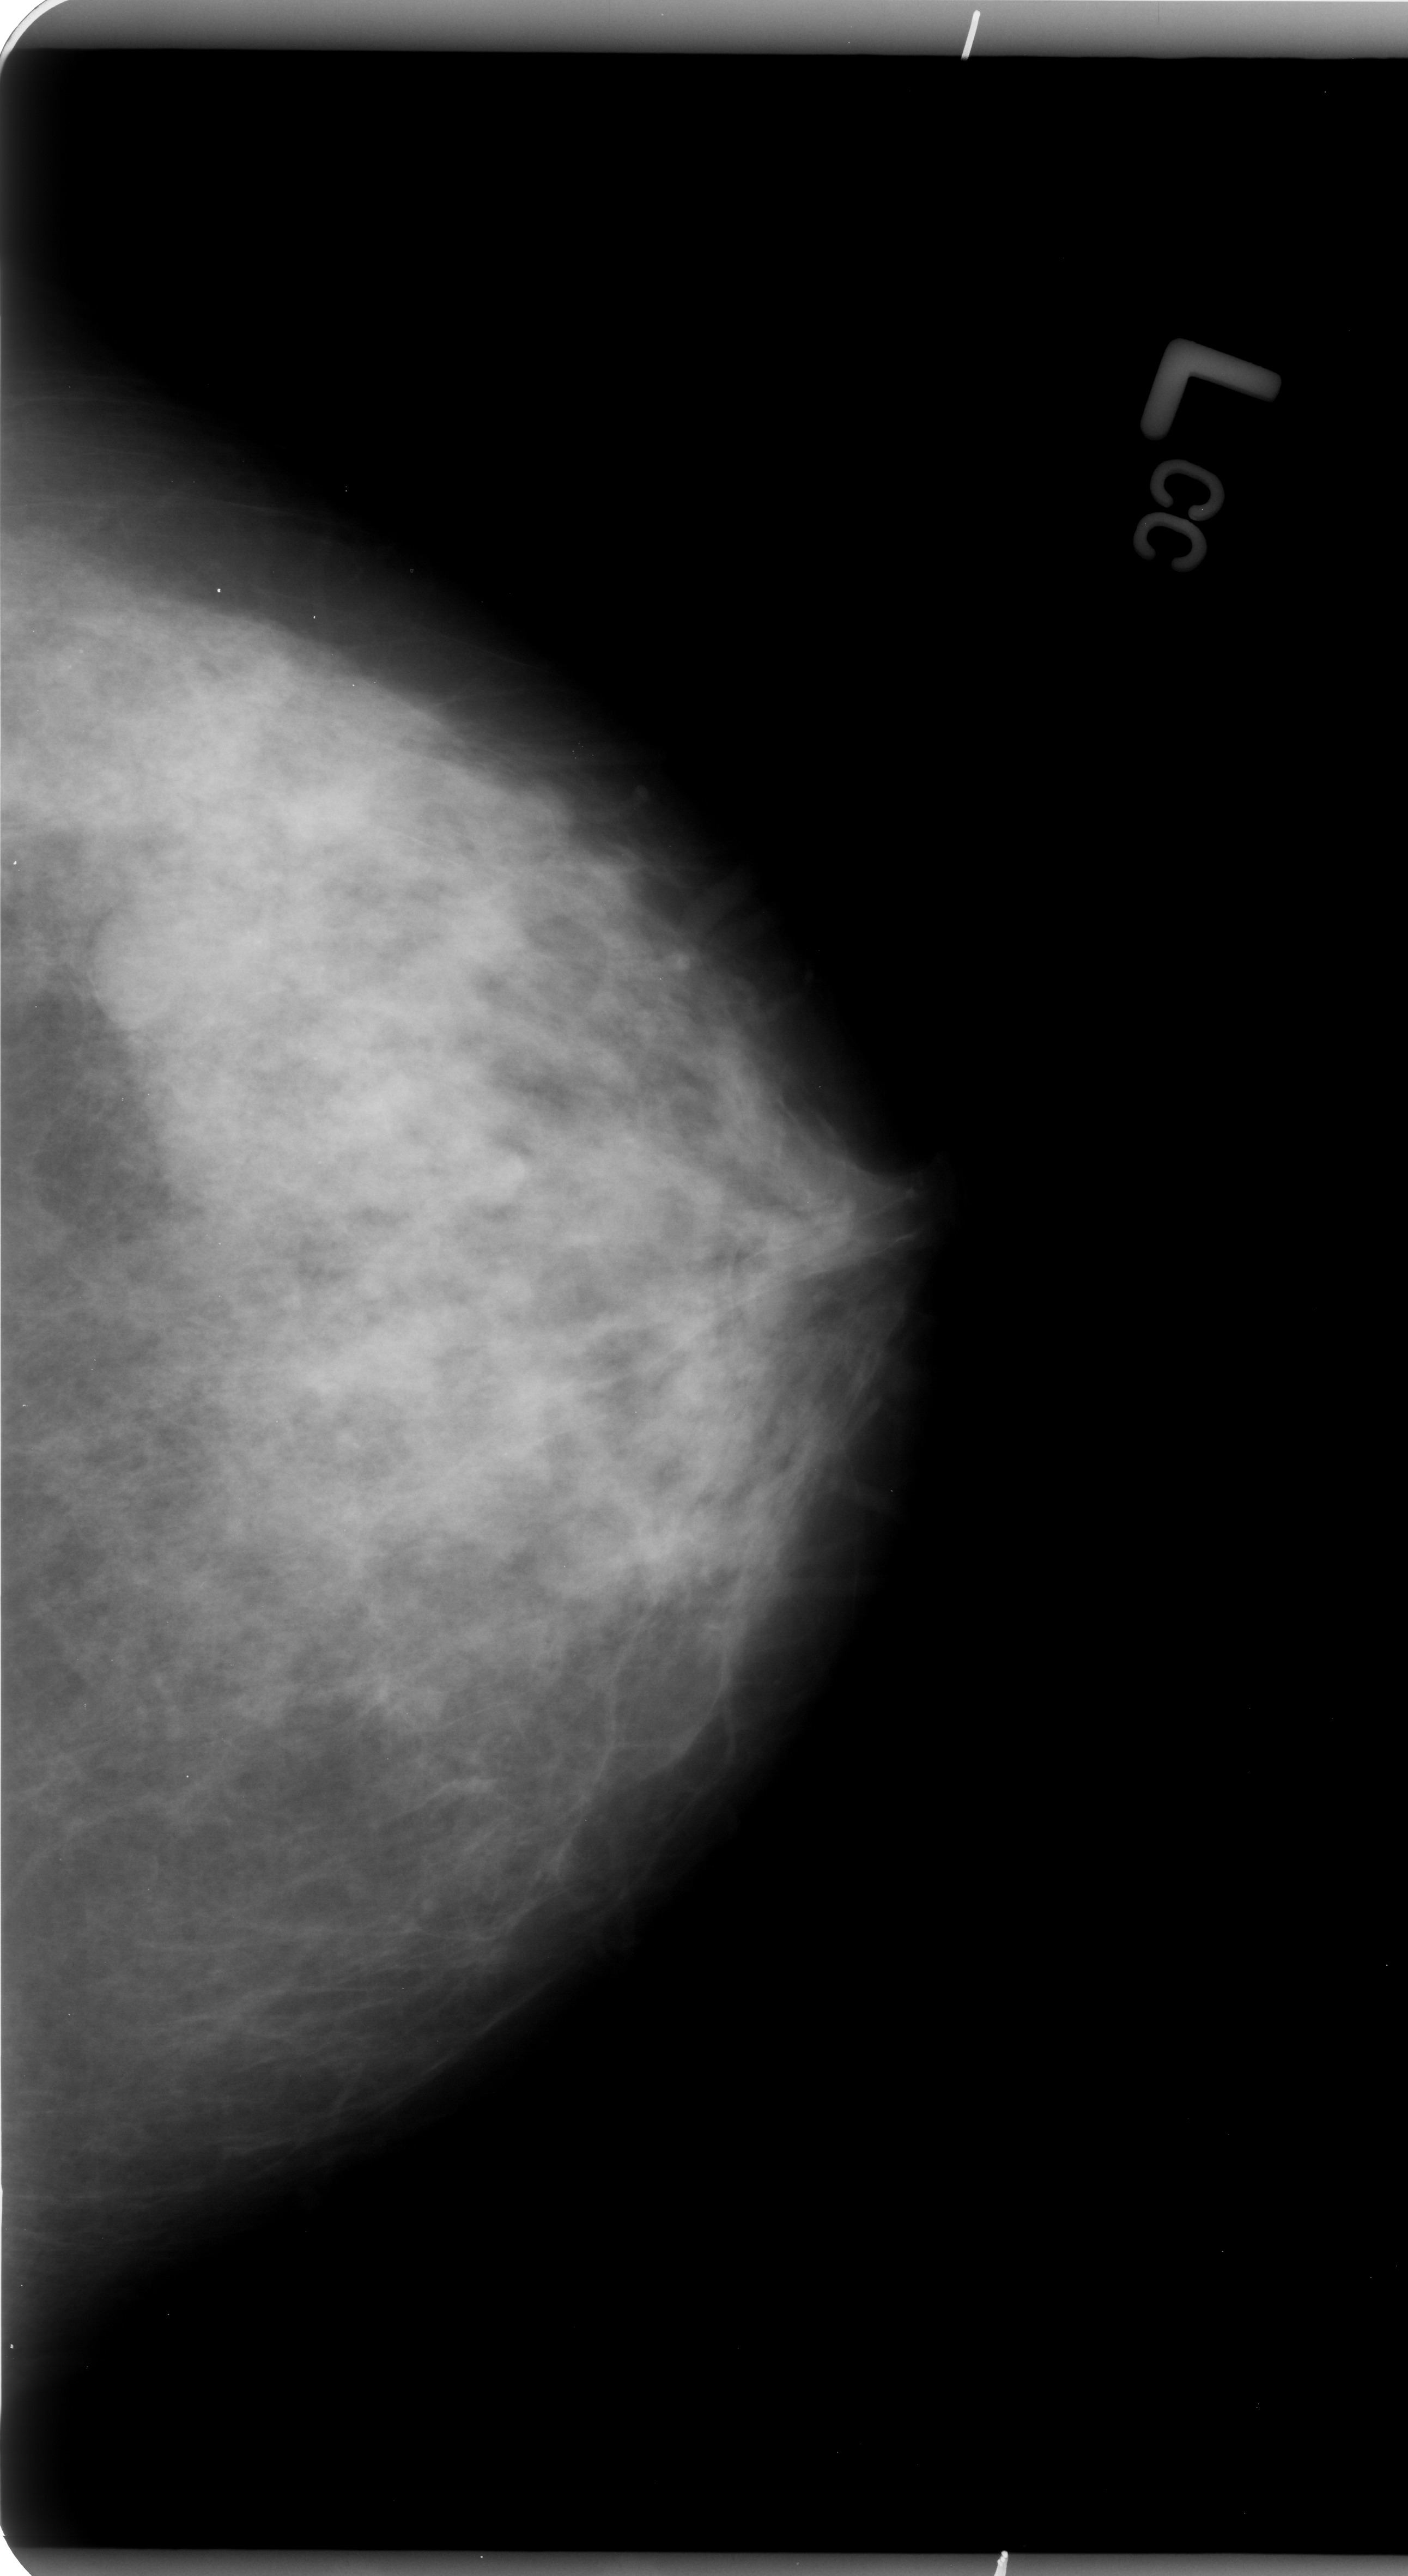
Digitized screen-film mammogram, left breast, CC view, breast composition: heterogeneously dense (BI-RADS density category 3 of 4).
- Mass, shape oval, margins circumscribed; BI-RADS assessment category 3; subtlety rating 3 on a 1 (subtle) to 5 (obvious) scale; pathology (as recorded): benign.